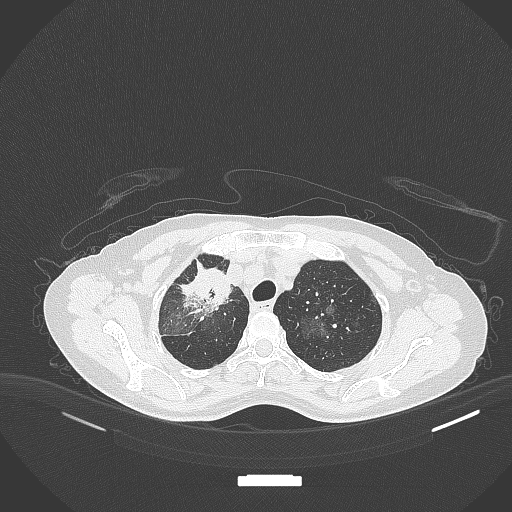
Chest CT, one axial slice. Position 266 of 284 along the scan axis. Reconstruction kernel B70f. 120 kVp. Lung window (W 1500 / L -600 HU). 1 mm slice thickness. 512 × 512 image matrix, field of view 400 × 400 mm. Patient: female, 59 years. Case-level facts recorded for this patient, not image findings: clinical TNM (as recorded): T3 N0 M0; histopathological grade: G1.
Structures marked on this image (rectangle marked by the reading radiologist):
- lung tumour (recorded histology: adenocarcinoma): bounding box (x1, y1, x2, y2) in pixels: (176, 262, 231, 319)